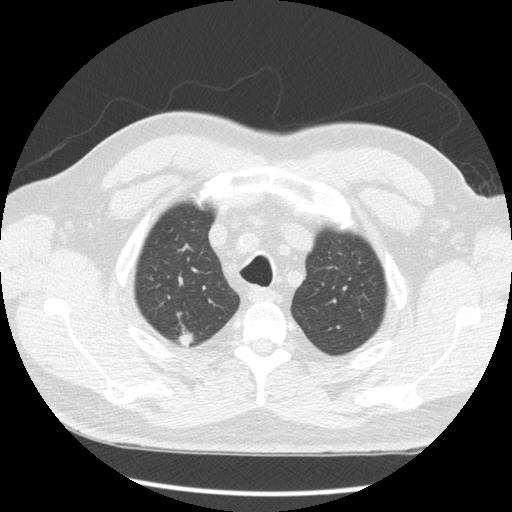
Low-dose screening chest CT, one axial slice; position 144 of 163 along the scan axis; reconstruction kernel STANDARD; 120 kVp; lung window (W 1500 / L -600 HU); 2.5 mm slice thickness; 512 × 512 image matrix.
Structures marked on this image (outlined manually by an expert reader):
- lesion 1 (tumor, upper lobe of right lung): bounding box <177,329,194,347> (left, top, right, bottom; pixels)